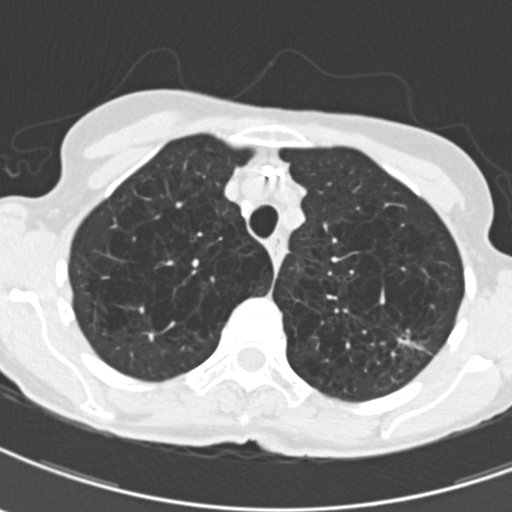
Axial slice from a low-dose chest CT screening exam. Third annual screen. Lung window (W 1500 / L -600 HU). 512 × 512 image matrix. Female participant, aged 71 years at enrolment.
Lesion marked by an expert reader, bounding box [x1, y1, x2, y2] px = [394, 320, 445, 366]. Reader record for this screening exam (exam-level; its link to the box is not recorded): non-calcified nodule or mass ≥4 mm, left upper lobe, 12 × 9 mm, spiculated (stellate) margins, mixed attenuation, pre-existing on the prior screen: yes; interval growth: yes. Official screen result: positive, other. Lung cancer was diagnosed 114 days after this screen: adenocarcinoma, NOS, left upper lobe, moderately differentiated (G2), stage IA (AJCC 6th edition), 12 mm at pathology.